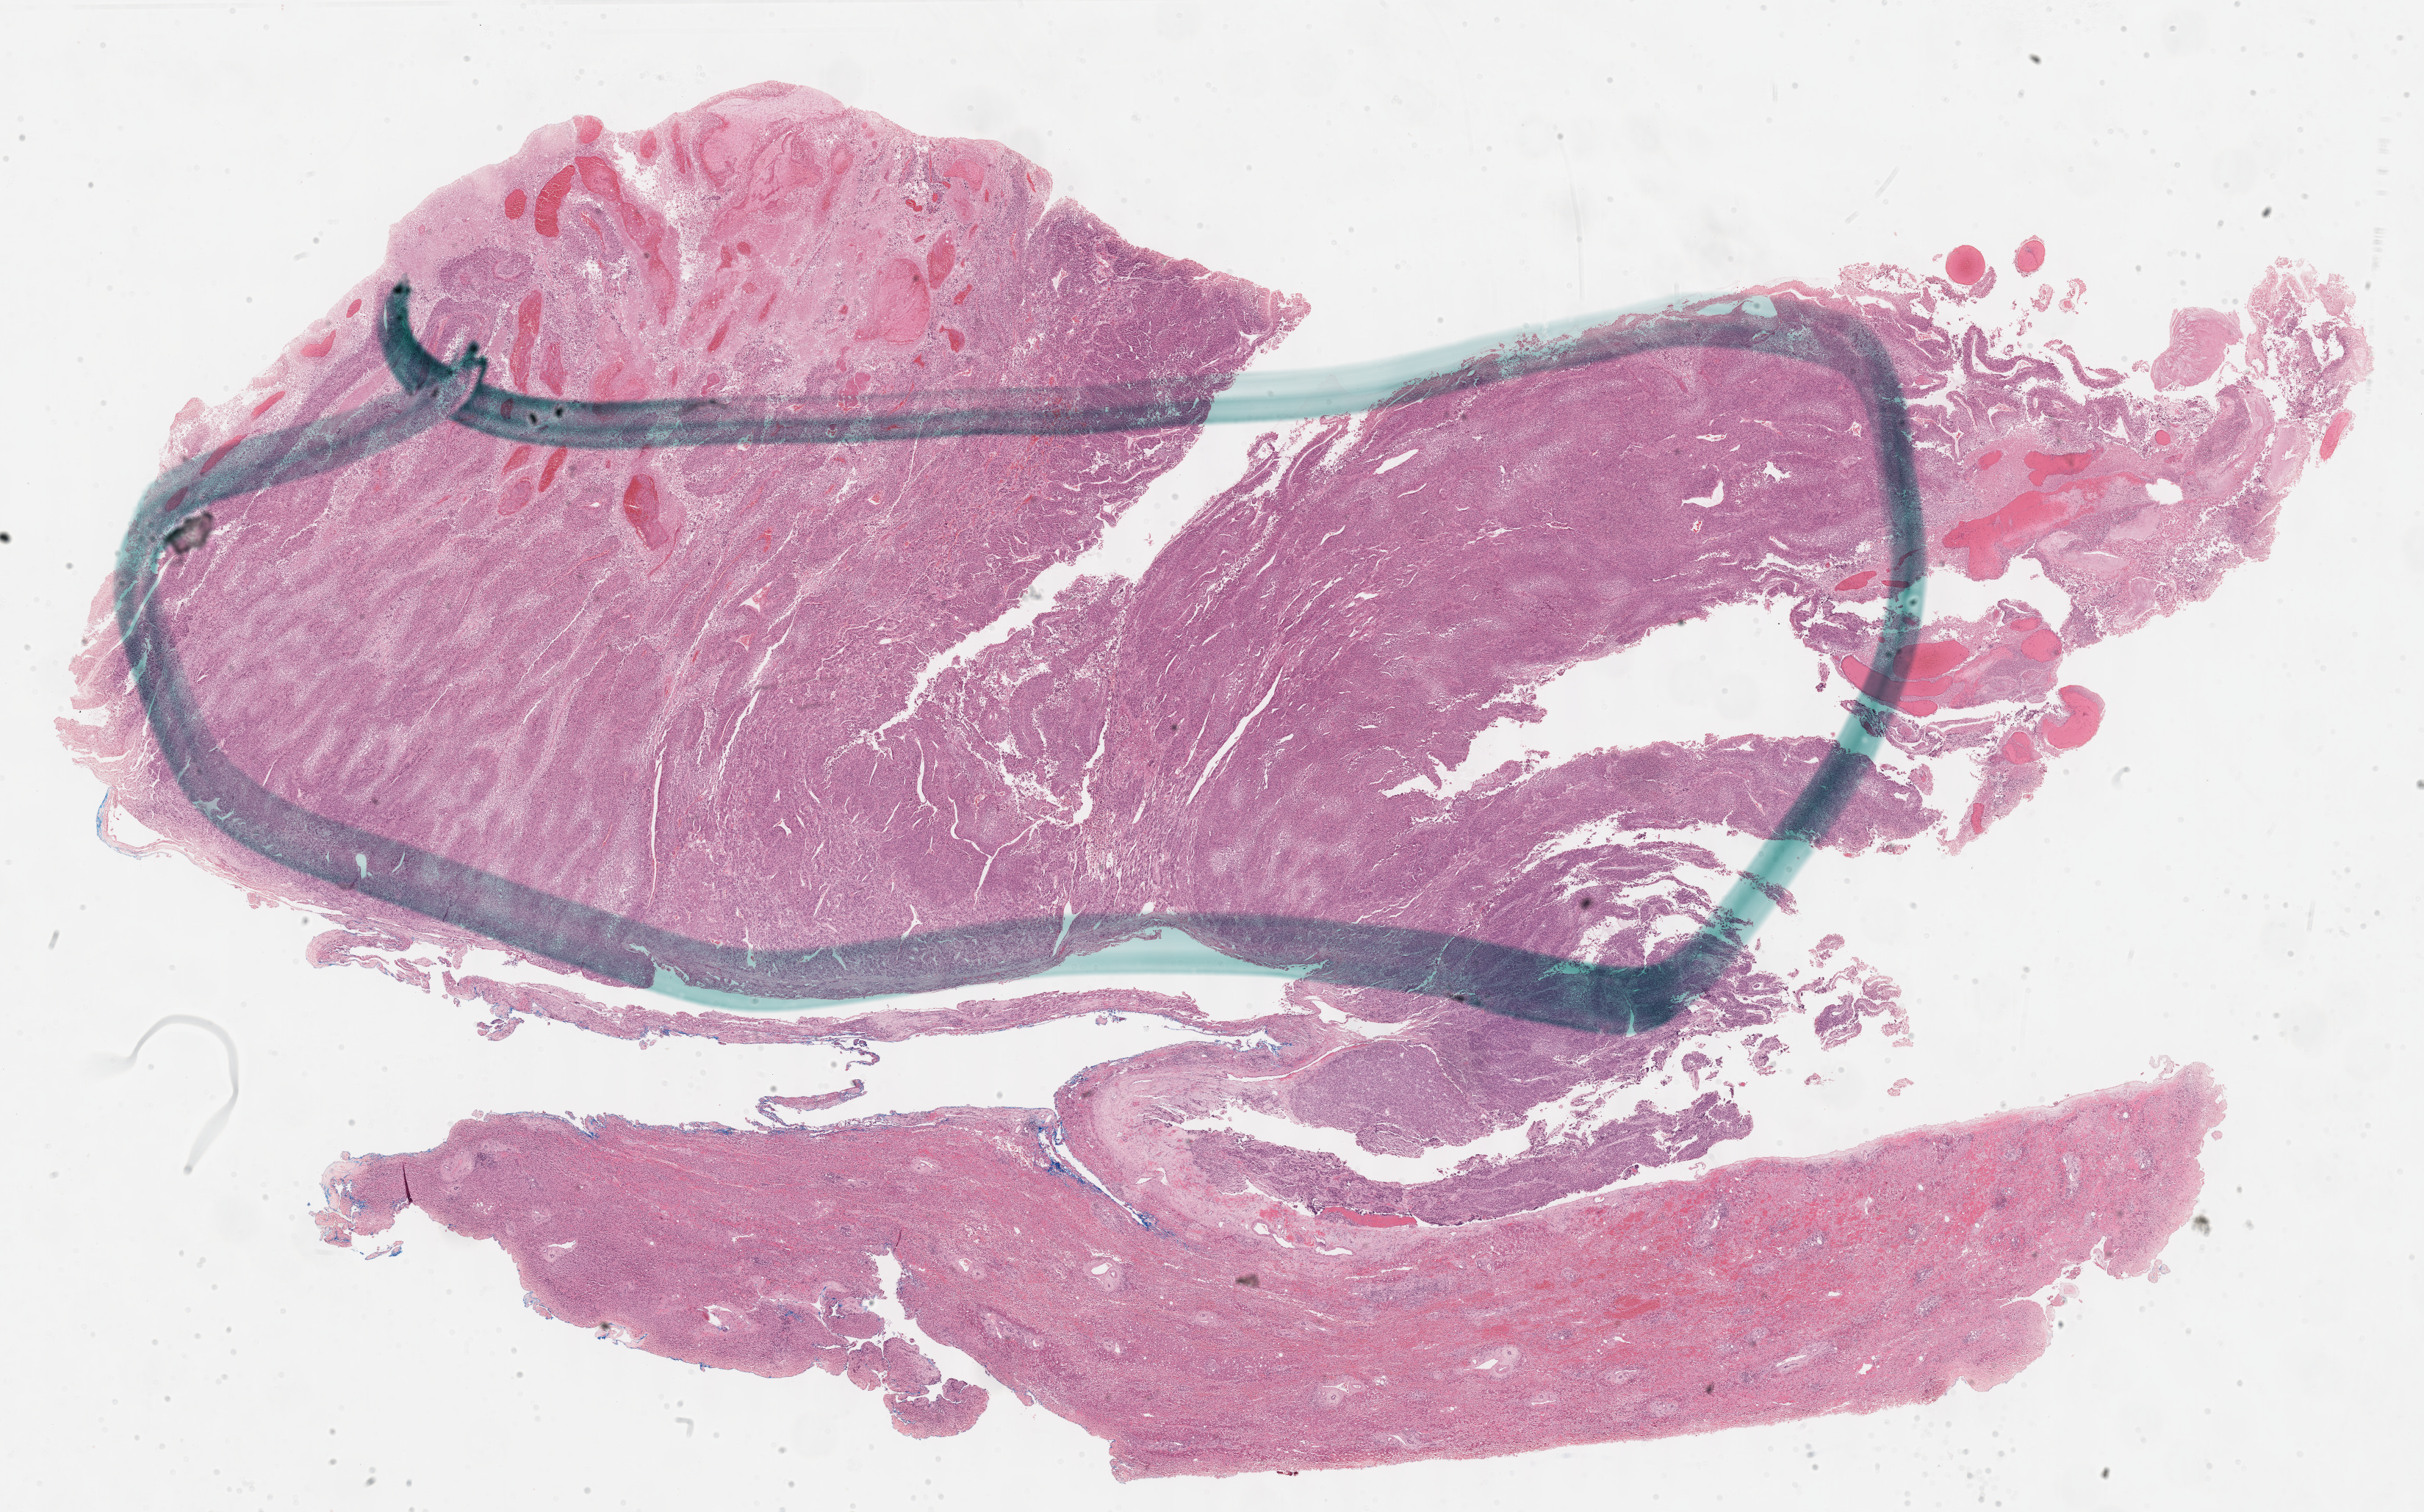
Whole-slide histology image, Hematoxylin and eosin (H&E) stained, shown as a low-resolution overview of the whole scanned area (about 26.7 x 16.6 mm). FFPE section. Sample: primary tumour, adrenal cortex. Patient: female, age at initial diagnosis 61 years.
- diagnosis: Adrenal cortical carcinoma (cortex of adrenal gland)
- laterality: right